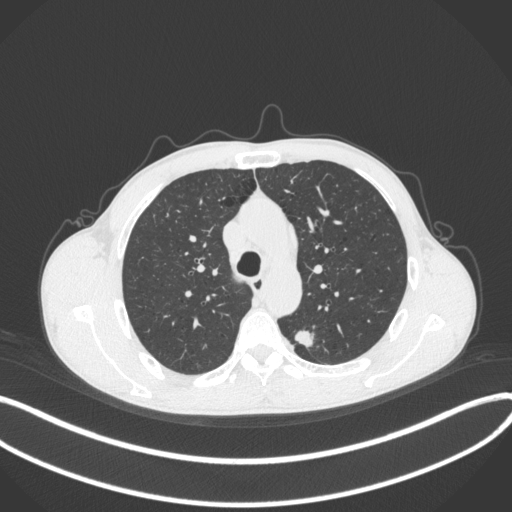
Chest CT, one axial slice. Slice 282 of 429 in the series (ordered by position). Reconstruction kernel B31f. 120 kVp. Lung window (W 1500 / L -600 HU). 1 mm slice thickness. 512 × 512 image matrix, field of view 400 × 400 mm. Male patient, age 51 years. From the clinical record (not read from this slice): clinical TNM (as recorded): T2a N1 M1.
Outlined on this slice (bounding box drawn by a radiologist):
- lung tumour (recorded histology: adenocarcinoma): bounding box (x1, y1, x2, y2) in pixels: (291, 327, 316, 349)